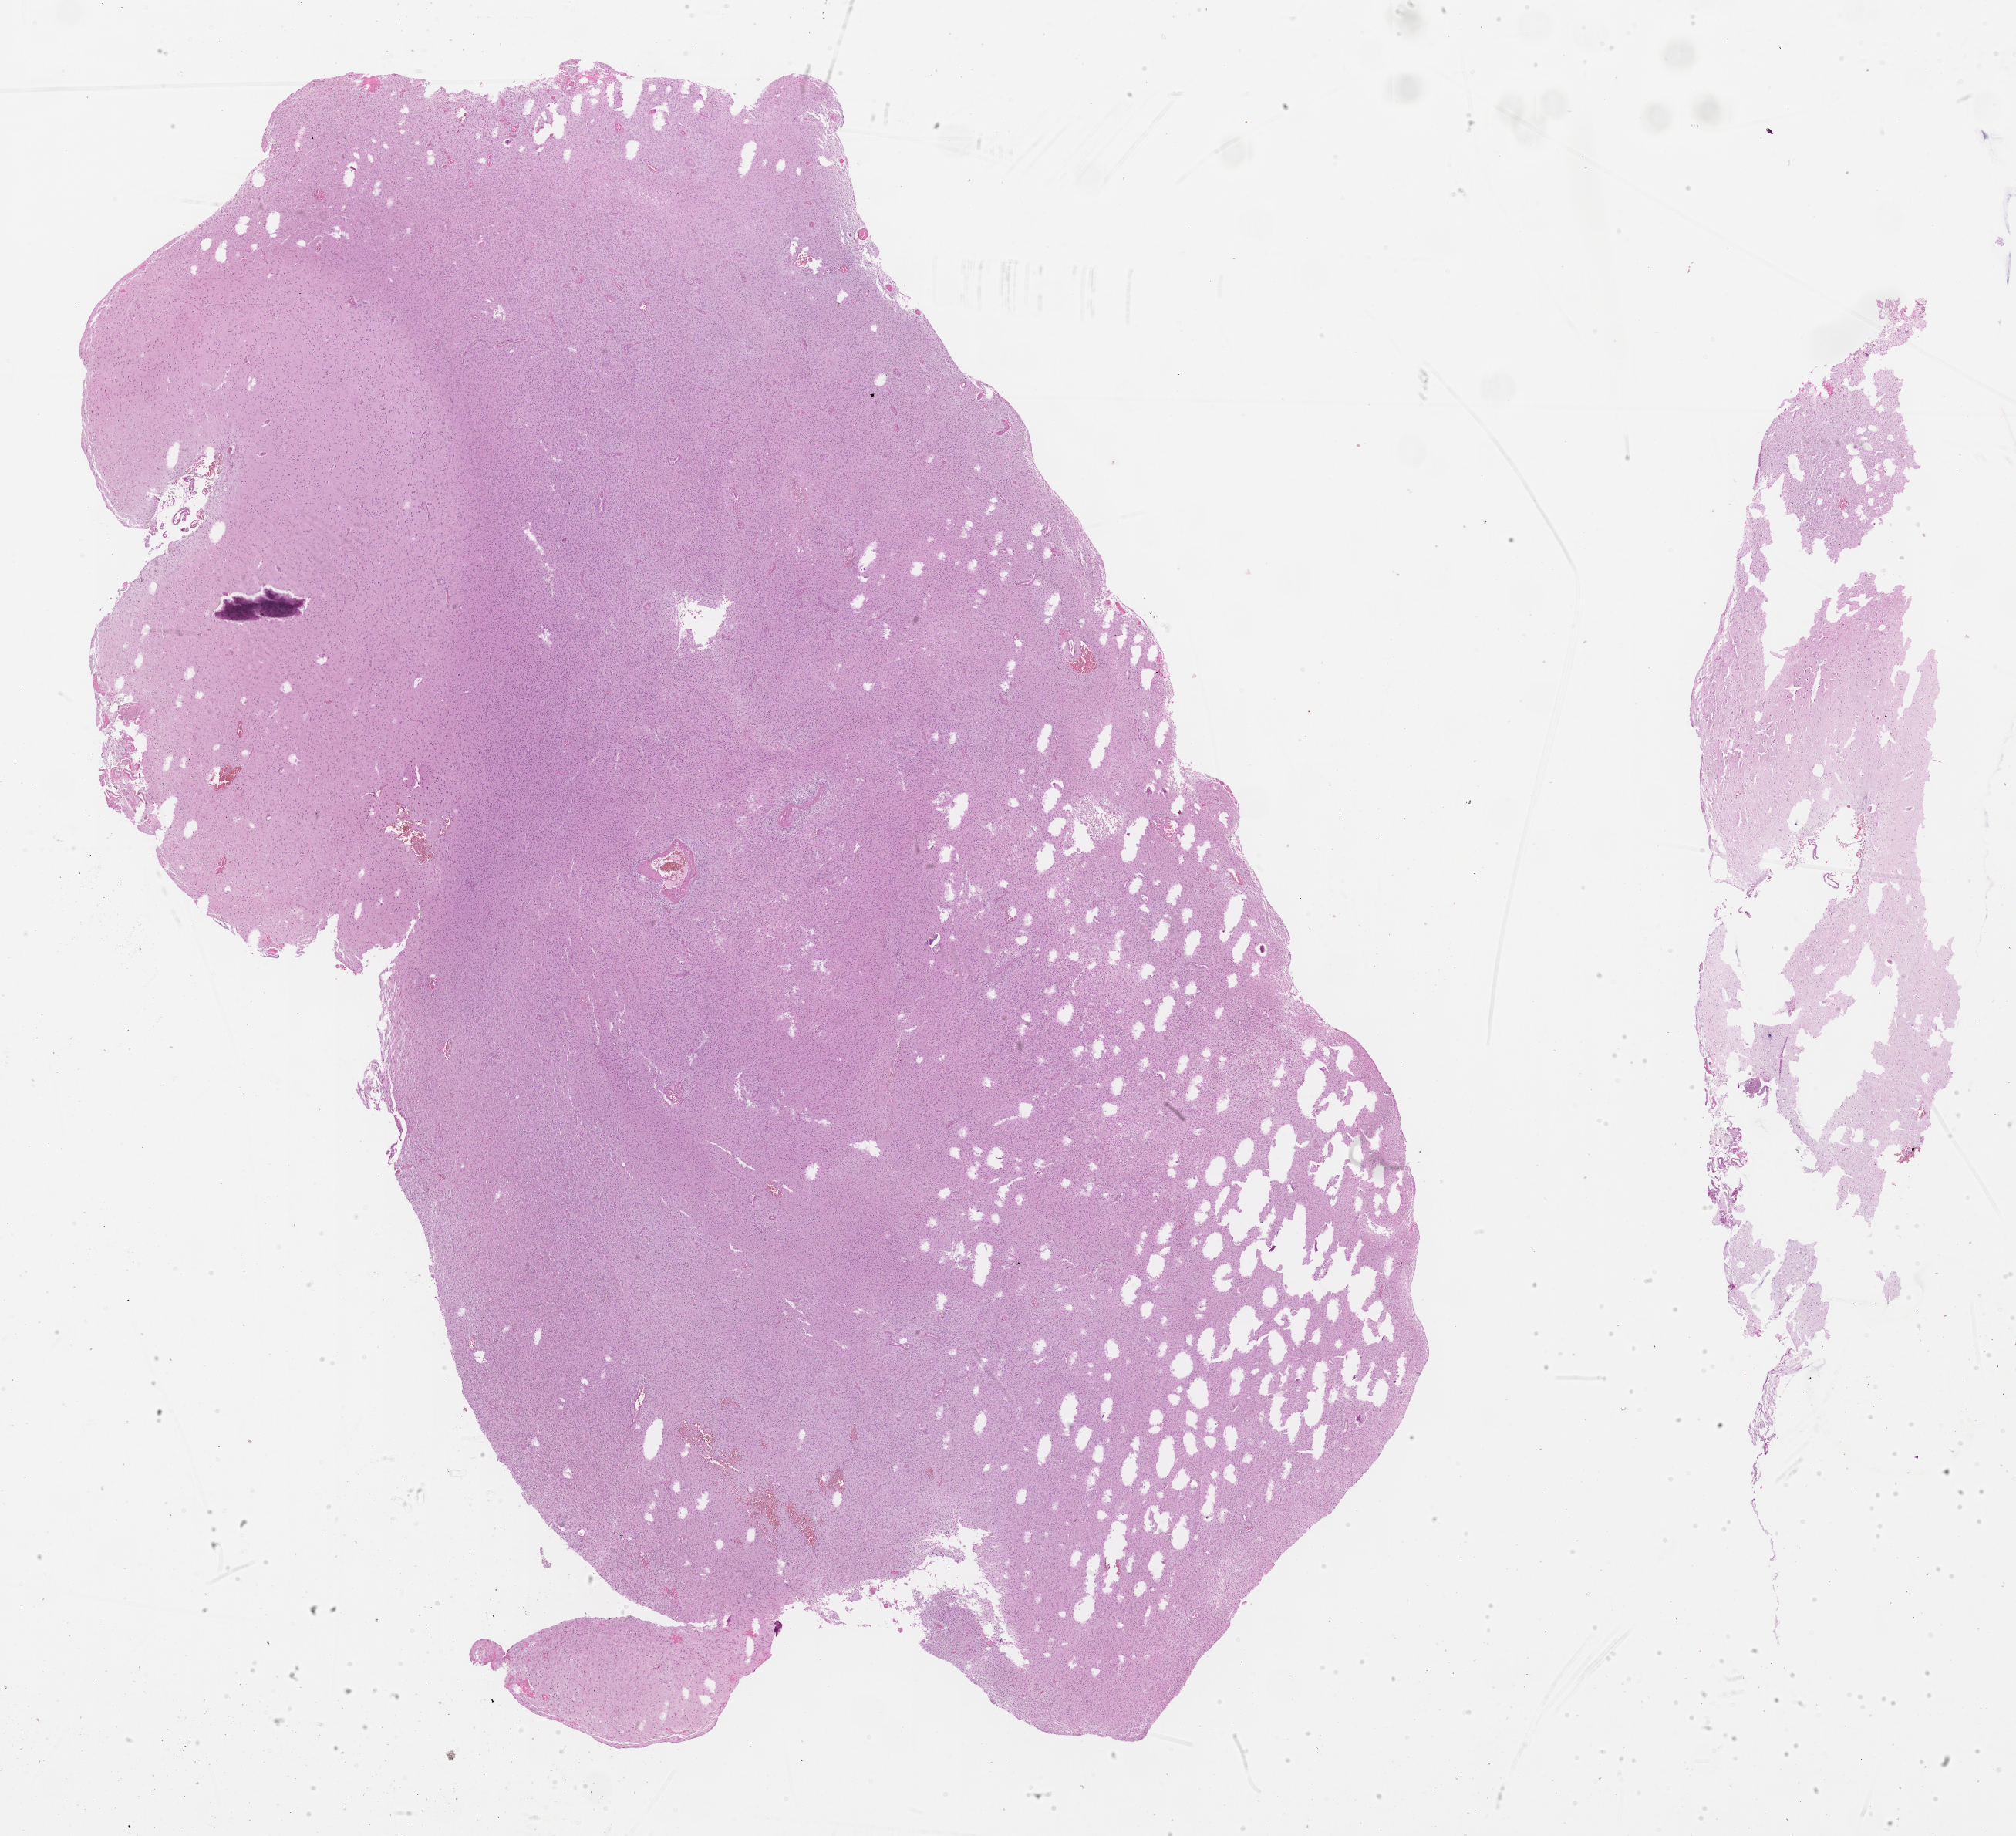
Digitized H&E-stained tissue section (whole slide), shown as a low-resolution overview of the whole scanned area (about 21.2 x 19.3 mm). FFPE section. Primary tumour sample from the brain. Patient: female, age at initial diagnosis 74 years.
* pathologic diagnosis: Glioblastoma